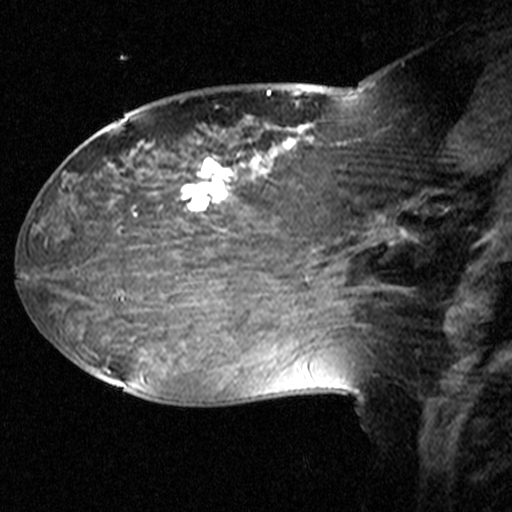
Breast MRI (dynamic contrast-enhanced), one sagittal slice. Position 21 of 44 along the scan axis. Dynamic contrast-enhanced study with each time point stored as its own series, time point 2 of 3 at this slice position (early post-contrast, ordered by acquisition time). 1.5 T. TE 4.5 ms, TR 11 ms. 3 mm slice thickness. 512 × 512 image matrix, field of view 240 × 240 mm. Female patient, age 38 years. Case-level facts recorded for this patient, not image findings: setting: breast cancer imaged before/during neoadjuvant chemotherapy; receptor status: HR-positive, HER2-negative.
Outlined on this slice (semi-automatically segmented with operator editing):
- analysis volume of interest (the breast-tissue region the enhancement analysis was run in; not a lesion): bounding box <124,106,405,245> (left, top, right, bottom; pixels)
- tumour enhancement mask (voxels above the 90 % enhancement threshold inside the analysis volume of interest): <181,126,309,210>